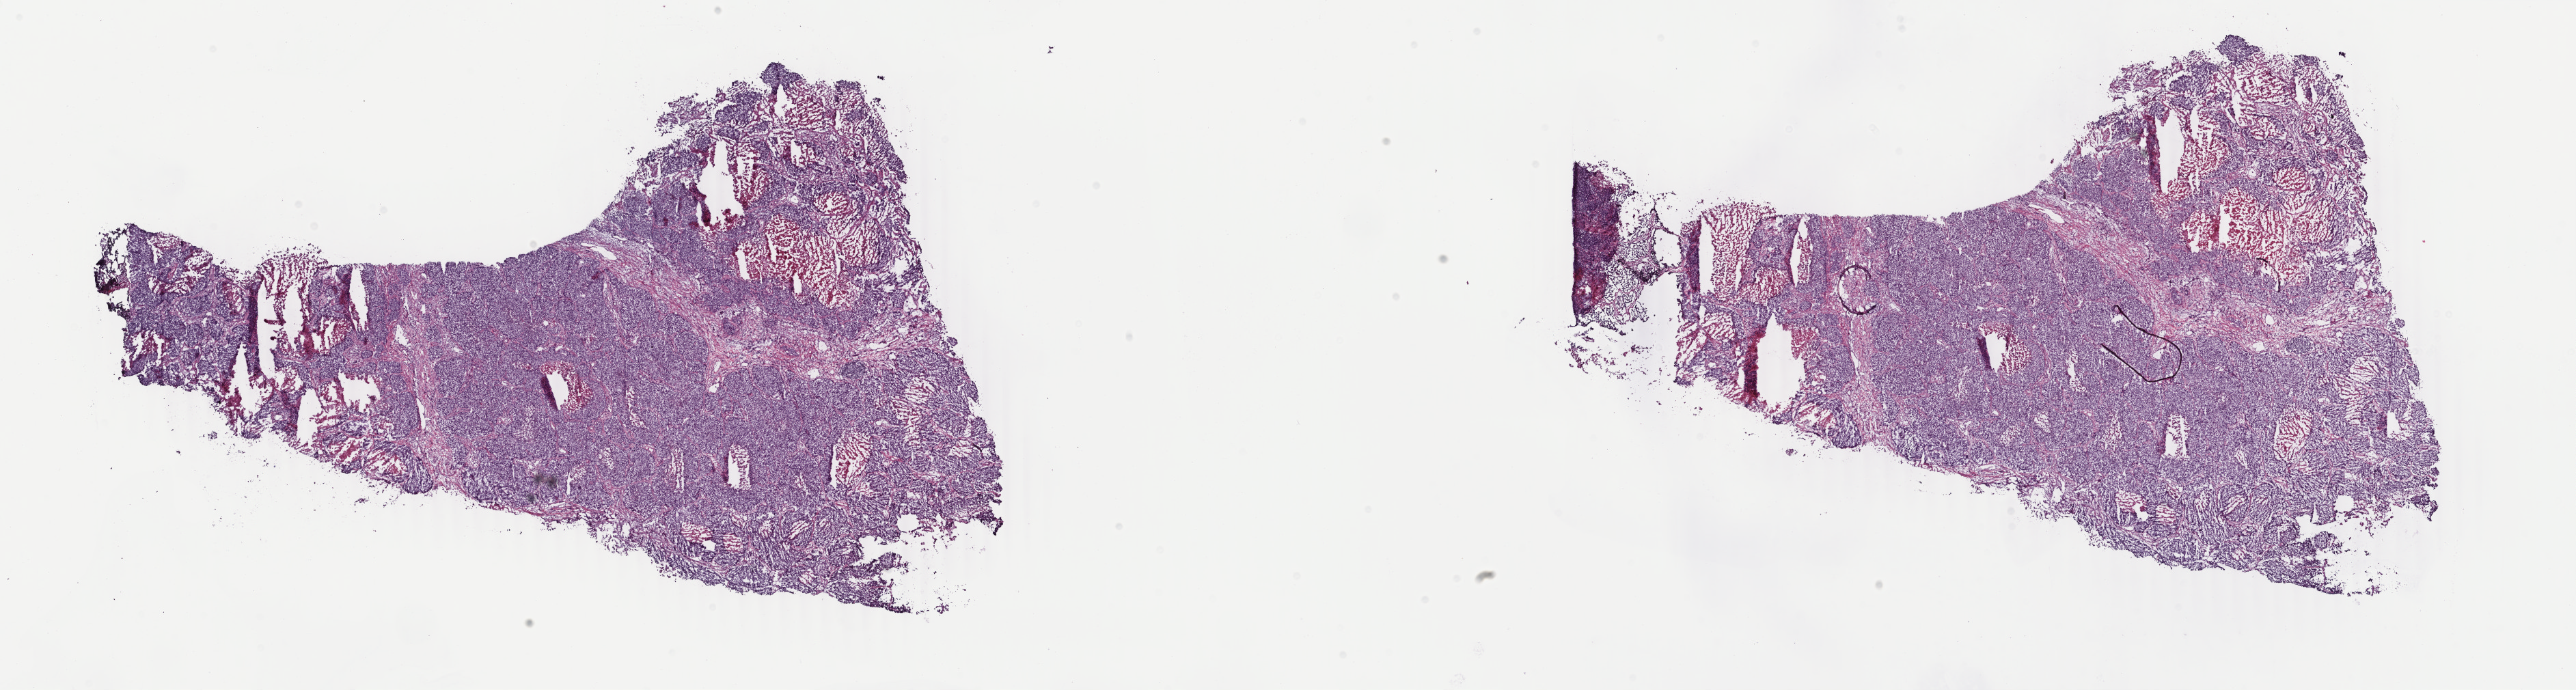
Whole-slide histology image, Hematoxylin and eosin (H&E) stained, low-resolution overview of the scanned area, about 30.0 x 8.0 mm, frozen section, primary tumour sample from the lung. Female, age 71 years at initial diagnosis. Composition of this section per pathologist review: tumour cells 85%, tumour nuclei 90%, normal cells 0%, stromal cells 0%, necrosis 15%. Infiltration values recorded for this section: lymphocyte infiltration 0%, monocyte infiltration 0%, neutrophil infiltration 0%.
• pathologic diagnosis: Squamous cell carcinoma, NOS (middle lobe, lung)
• laterality: right
• AJCC pathologic stage: III (6th edition)